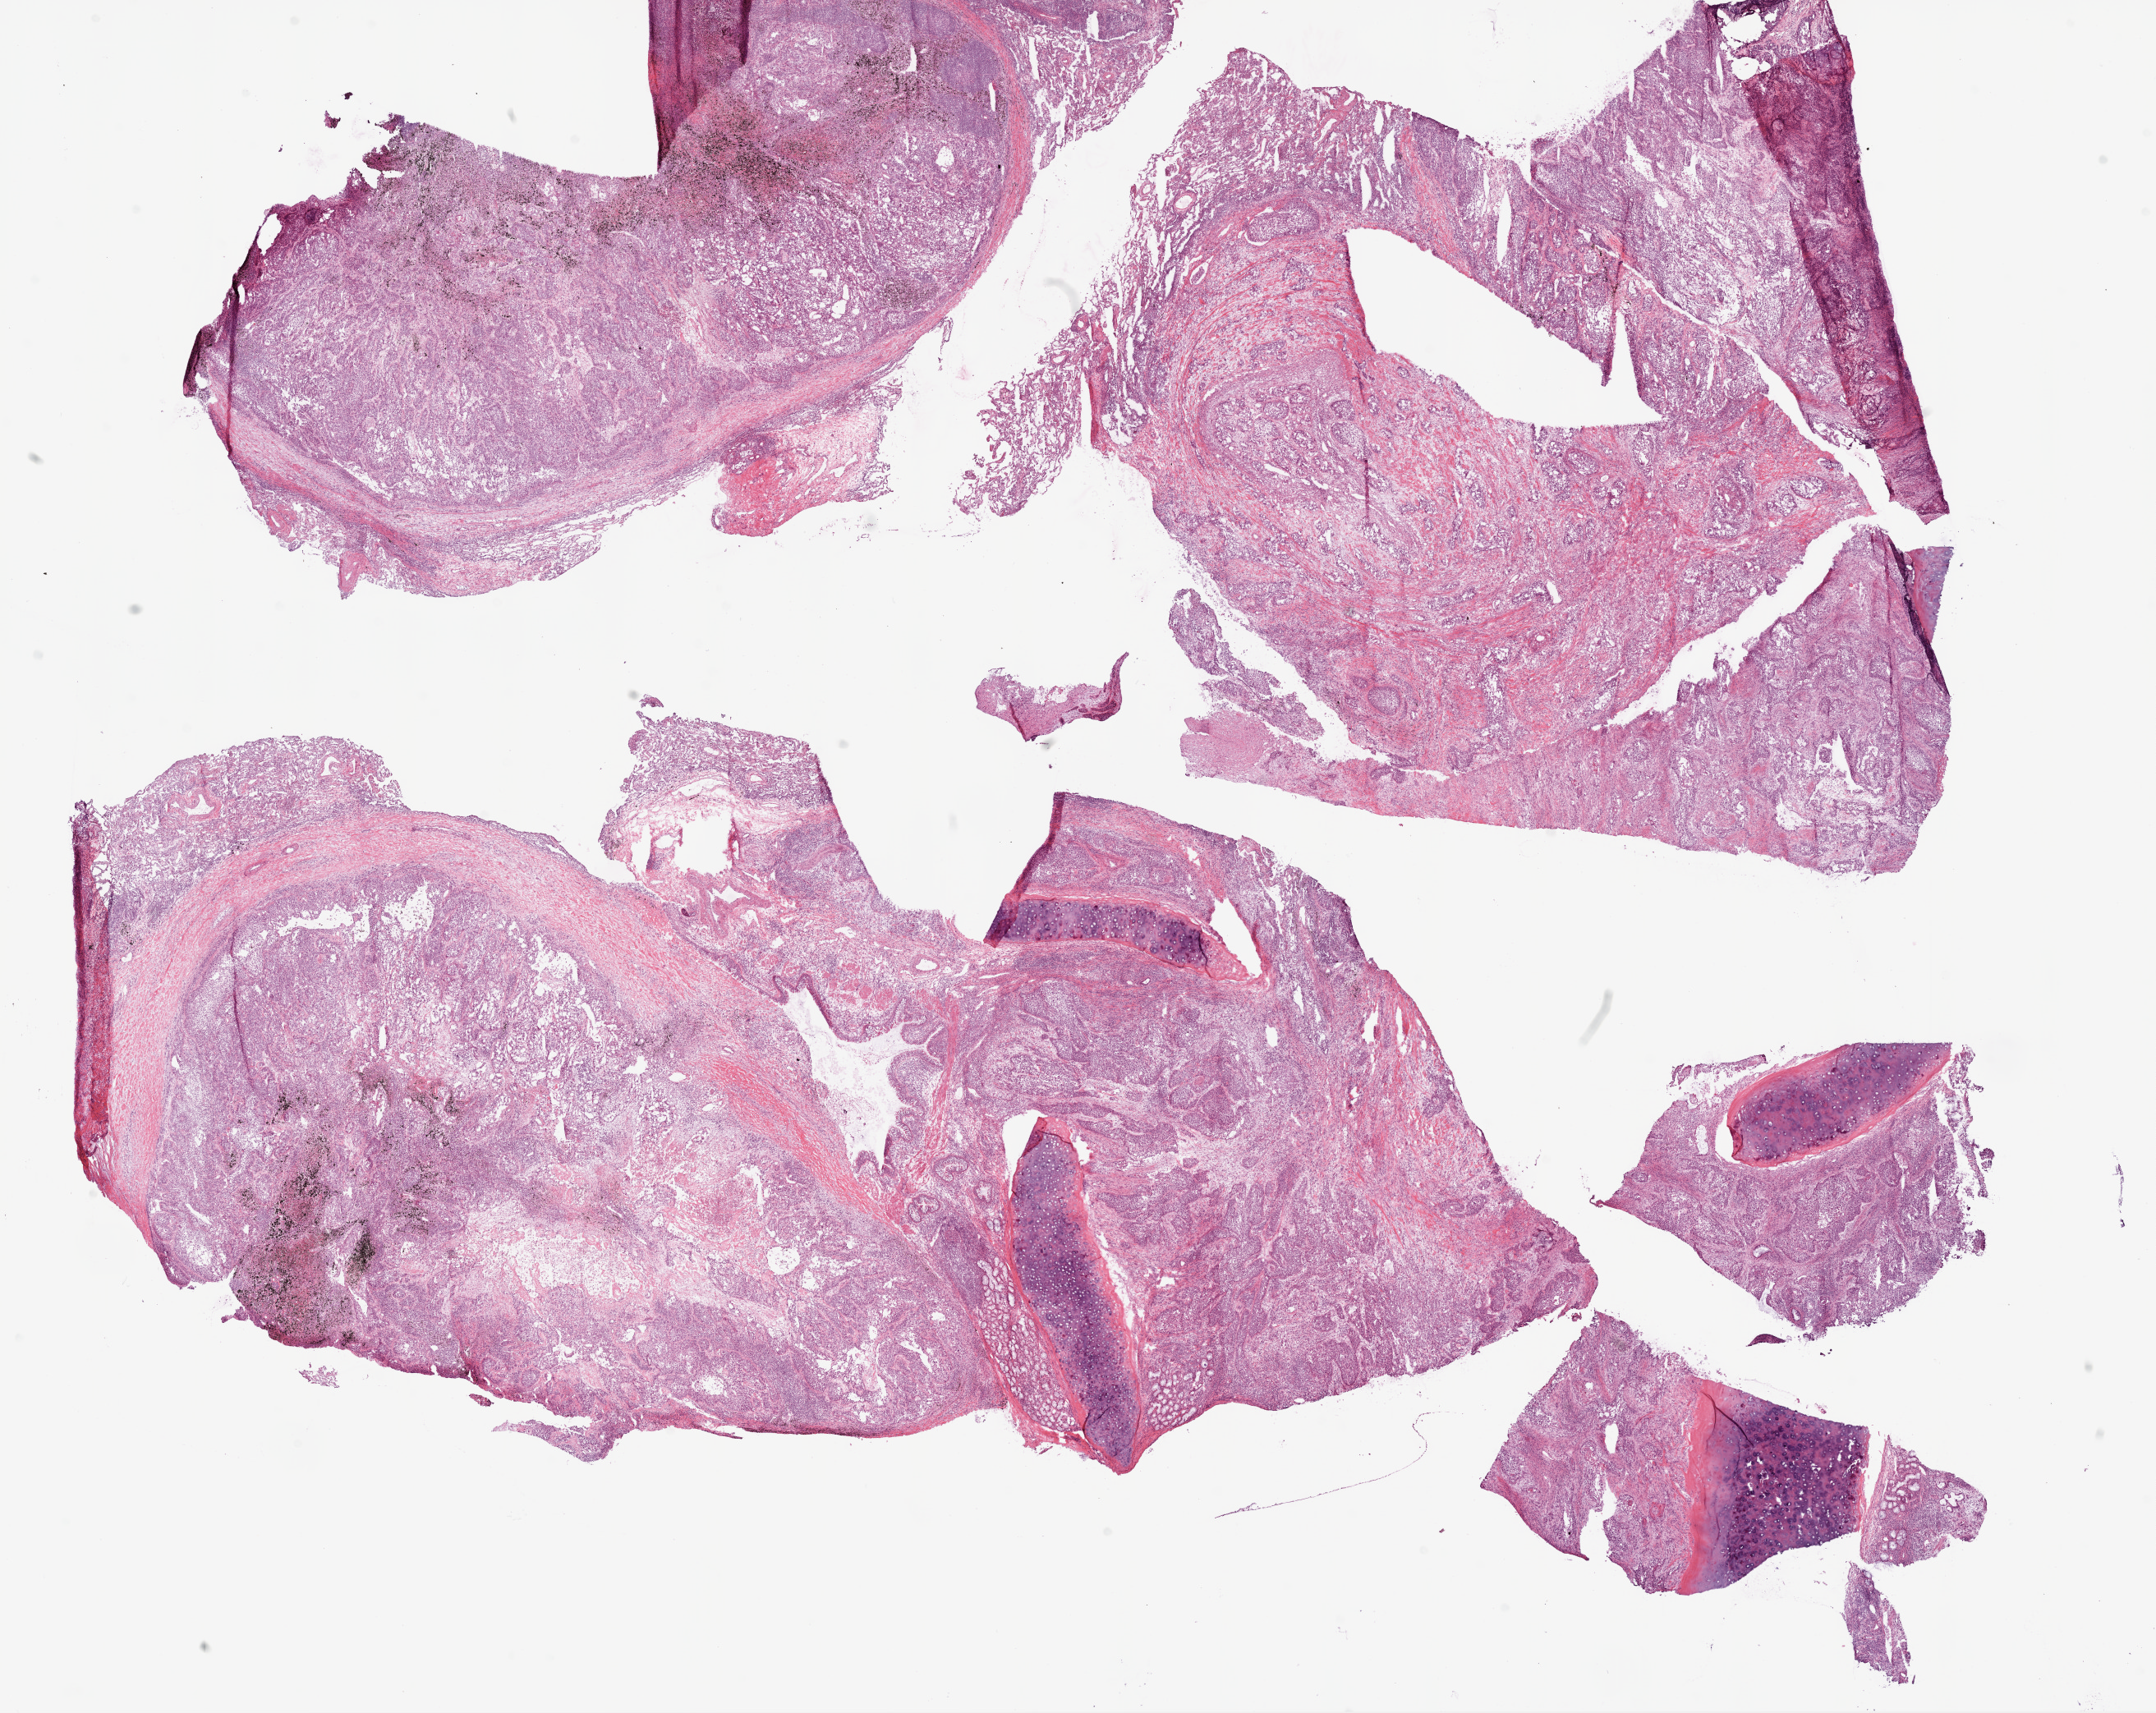
Whole-slide histology image, H&E-stained — a low-resolution overview of the entire scanned area, about 21.1 x 16.7 mm. Frozen section from the bottom of the tissue portion. Sample: primary tumour, lung. Patient: male, age at initial diagnosis 67 years. Slide review estimates, as recorded: tumour cells 59%, tumour nuclei 70%, normal cells 8%, stromal cells 30%, necrosis 3%.
• pathologic diagnosis: Squamous cell carcinoma, NOS (lower lobe, lung)
• AJCC pathologic stage: IIIA